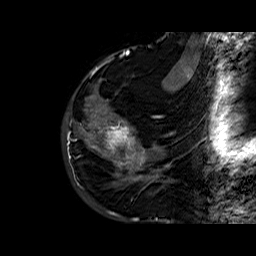
Breast MRI (dynamic contrast-enhanced), one sagittal slice. Position 16 of 60 along the scan axis. Dynamic contrast-enhanced series, time point 2 of 6 at this slice position (early post-contrast). 1.5 T. TE 6.4 ms, TR 32.8 ms. 4 mm slice thickness. 256 × 256 image matrix. Female patient. Case-level facts recorded for this patient, not image findings: setting: breast cancer imaged before/during neoadjuvant chemotherapy; receptor status: HR-positive, HER2-negative.
Outlined on this slice (semi-automatically segmented with operator editing):
- analysis volume of interest (the breast-tissue region the enhancement analysis was run in; not a lesion): box from (x=86, y=77) to (x=163, y=177) px
- tumour enhancement mask (voxels above the 100 % enhancement threshold inside the analysis volume of interest): (x=105, y=123)–(x=145, y=165)